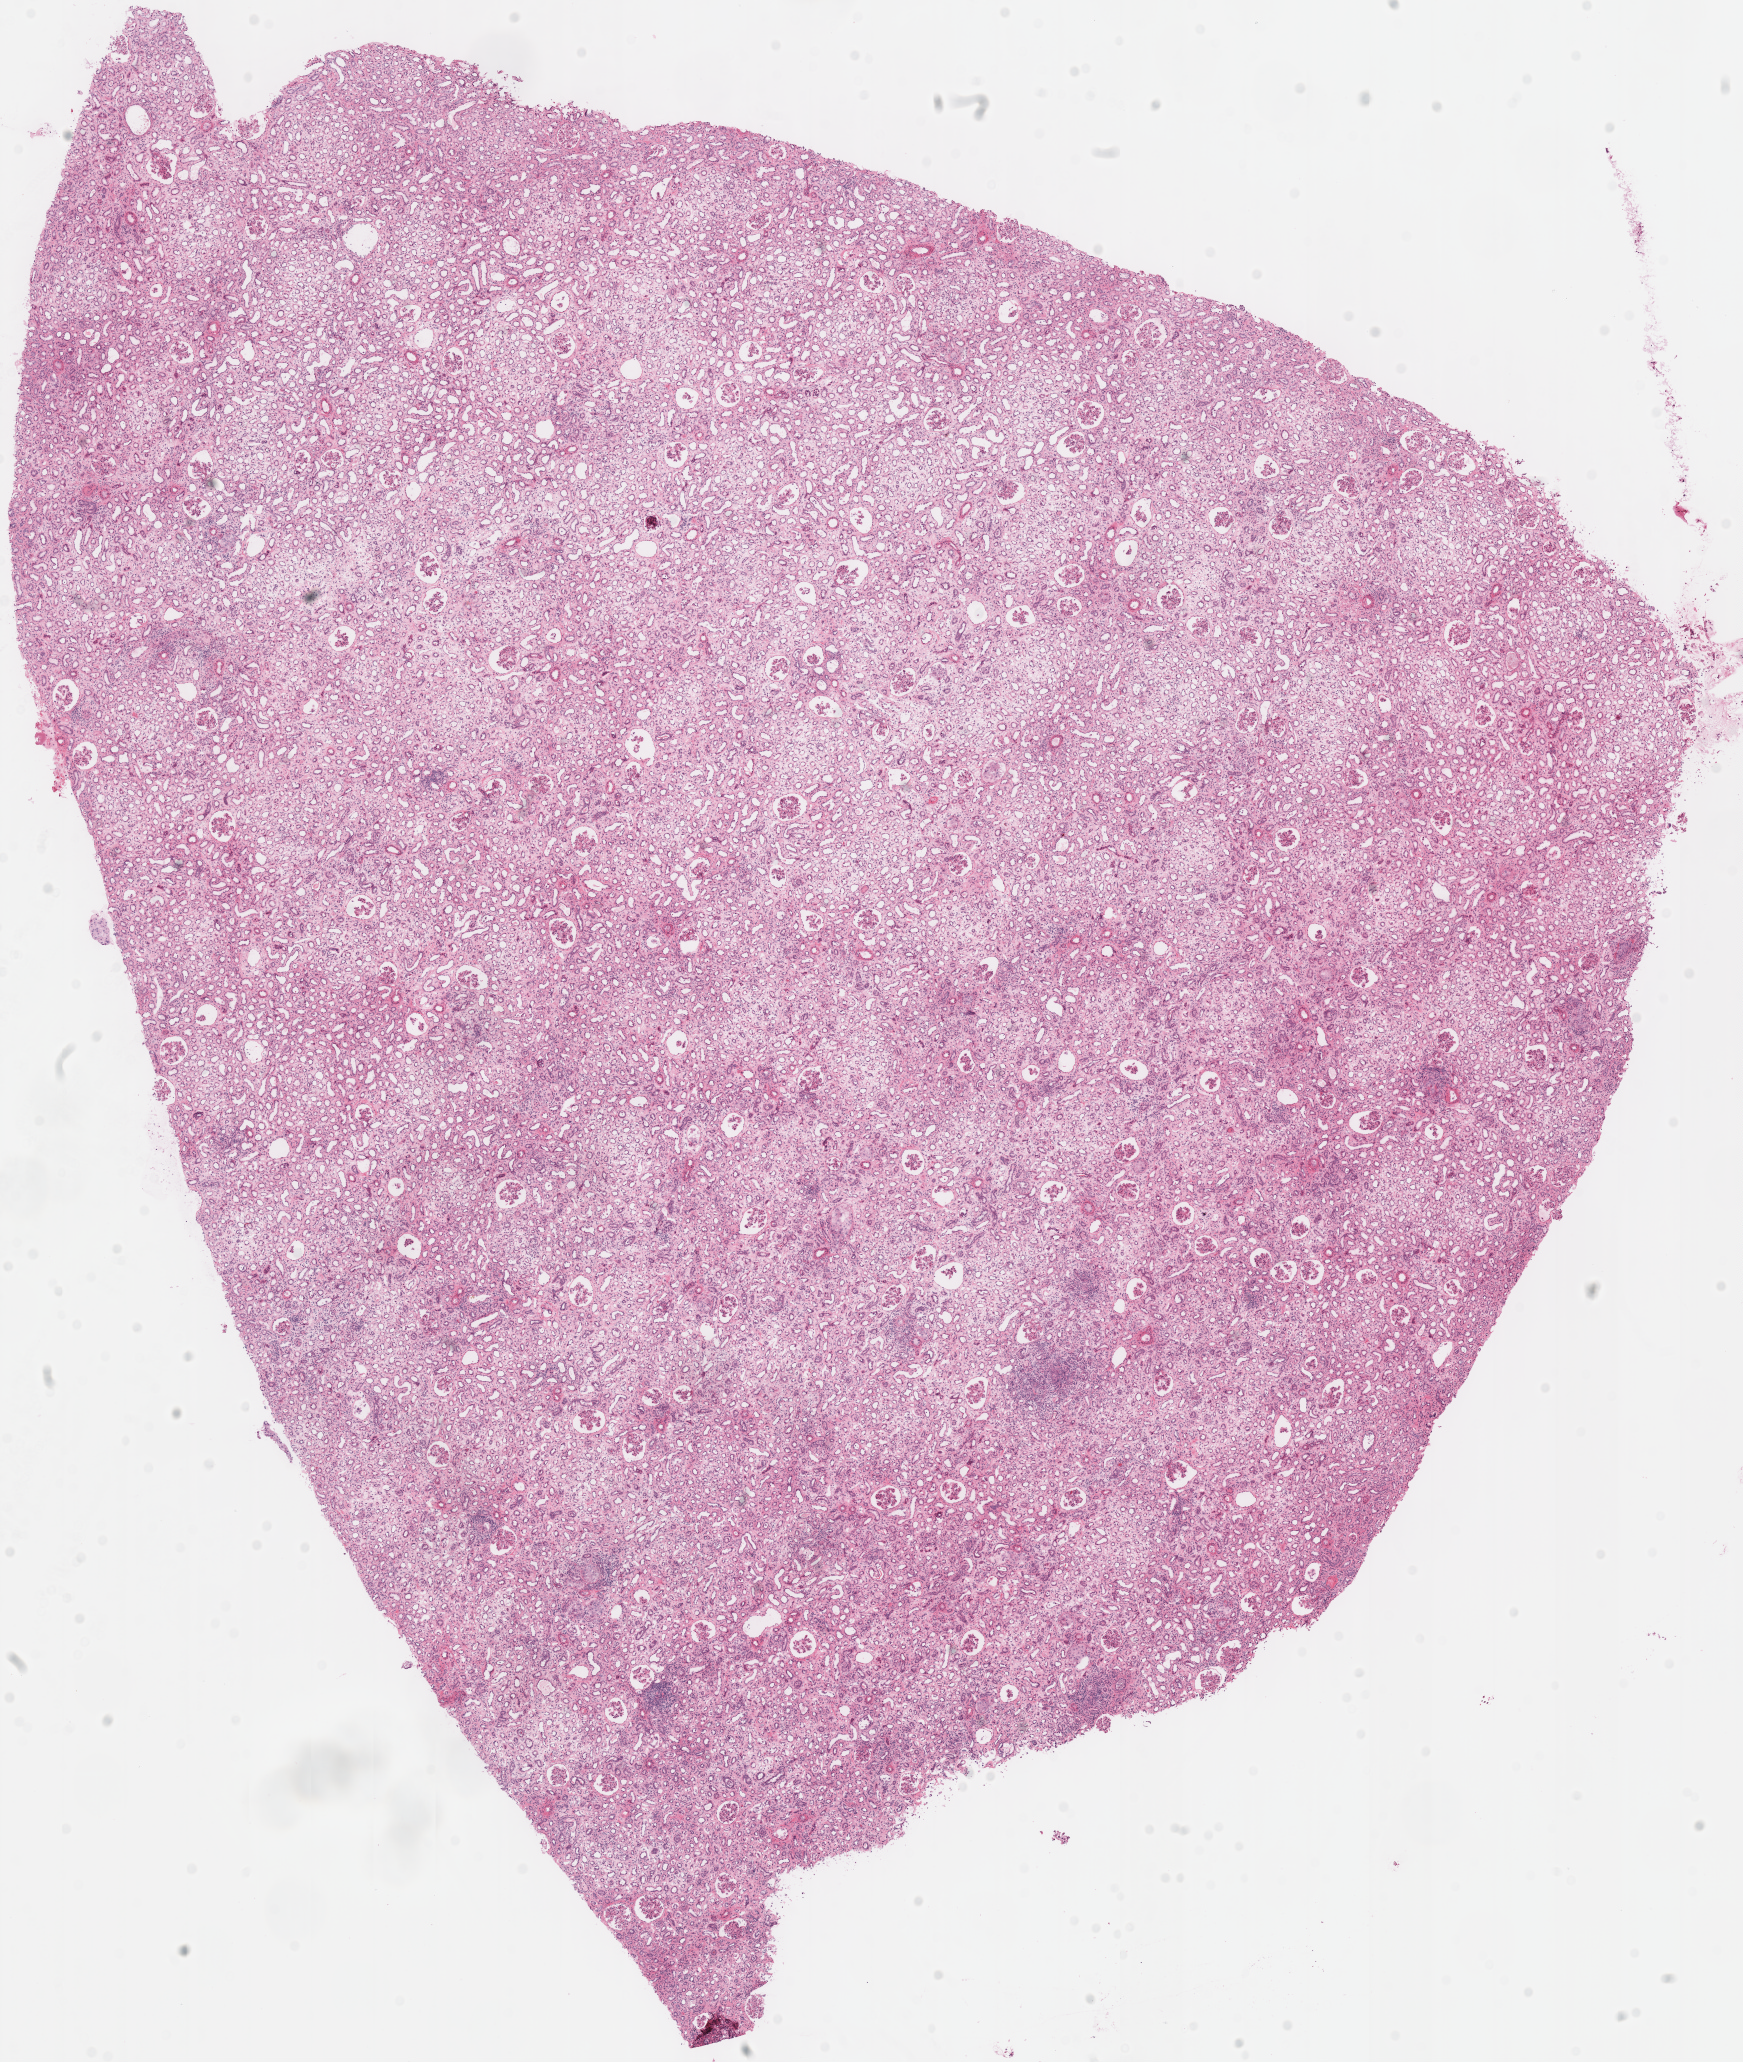
H&E whole-slide image, shown as a low-resolution overview of the whole scanned area (about 13.7 x 16.2 mm, acquisition: 40x scan), frozen section, solid tissue normal (non-tumour tissue) sample from the kidney. Patient: female, age at initial diagnosis 51 years. Inflammatory infiltration, as recorded: lymphocyte infiltration 5%, monocyte infiltration 0%, neutrophil infiltration 0%.
* this section: solid tissue normal sample (biorepository sample class)
* patient diagnosis: Renal cell carcinoma, chromophobe type